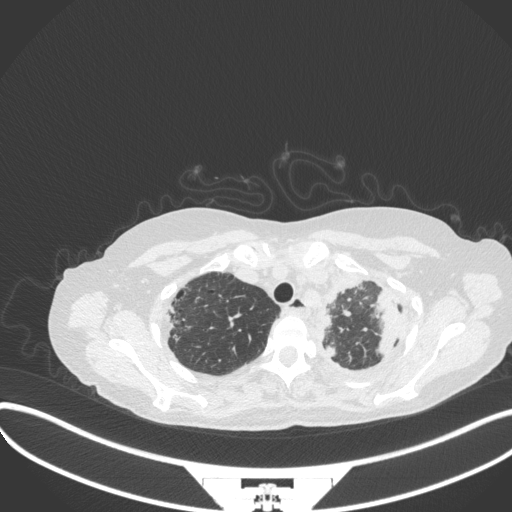
Chest CT, one axial slice; position 287 of 373 along the scan axis; 120 kVp; lung window (W 1500 / L -600 HU); 1 mm slice thickness; 512 × 512 image matrix. Patient: female, 56 years. From the clinical record (not read from this slice): clinical TNM (as recorded): T1 N0 M0.
Annotated regions visible in this slice (rectangle marked by the reading radiologist):
- lung tumour (recorded histology: adenocarcinoma): bounding box <369,290,400,364> (left, top, right, bottom; pixels)